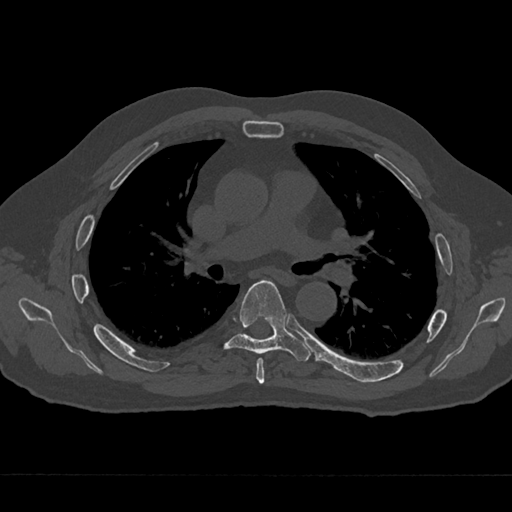
CT including the spine, one axial slice; slice 430 of 797 in the series (ordered by position); 120 kVp; bone window (W 1800 / L 400 HU); 512 × 512 image matrix, field of view 377 × 377 mm. Patient: male, 75 years. Case-level facts recorded for this patient, not image findings: primary cancer: renal; vertebrae with lytic lesions (as recorded): T4.
Structures marked on this image (semi-automatic segmentation, software-assisted and operator-edited):
- T5 vertebra: bounding box [x1, y1, x2, y2] px = [256, 358, 265, 384]
- T6 vertebra: [218, 280, 310, 361]